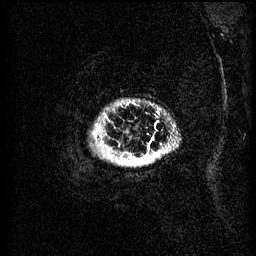
Breast MRI (dynamic contrast-enhanced), one sagittal slice. Slice 60 of 60 in the series (ordered by position). 3 images stored at this slice position (order not interpretable as contrast timing). 1.5 T. TE 4.2 ms, TR 11 ms. 256 × 256 image matrix, field of view 220 × 220 mm. Female patient, age 51 years.
Outlined on this slice (semi-automatically segmented with operator editing):
- analysis volume of interest (the breast-tissue region the enhancement analysis was run in; not a lesion): box from (x=111, y=104) to (x=158, y=165) px
- tumour enhancement mask (voxels above the 70 % enhancement threshold inside the analysis volume of interest): (x=131, y=156)–(x=149, y=163)